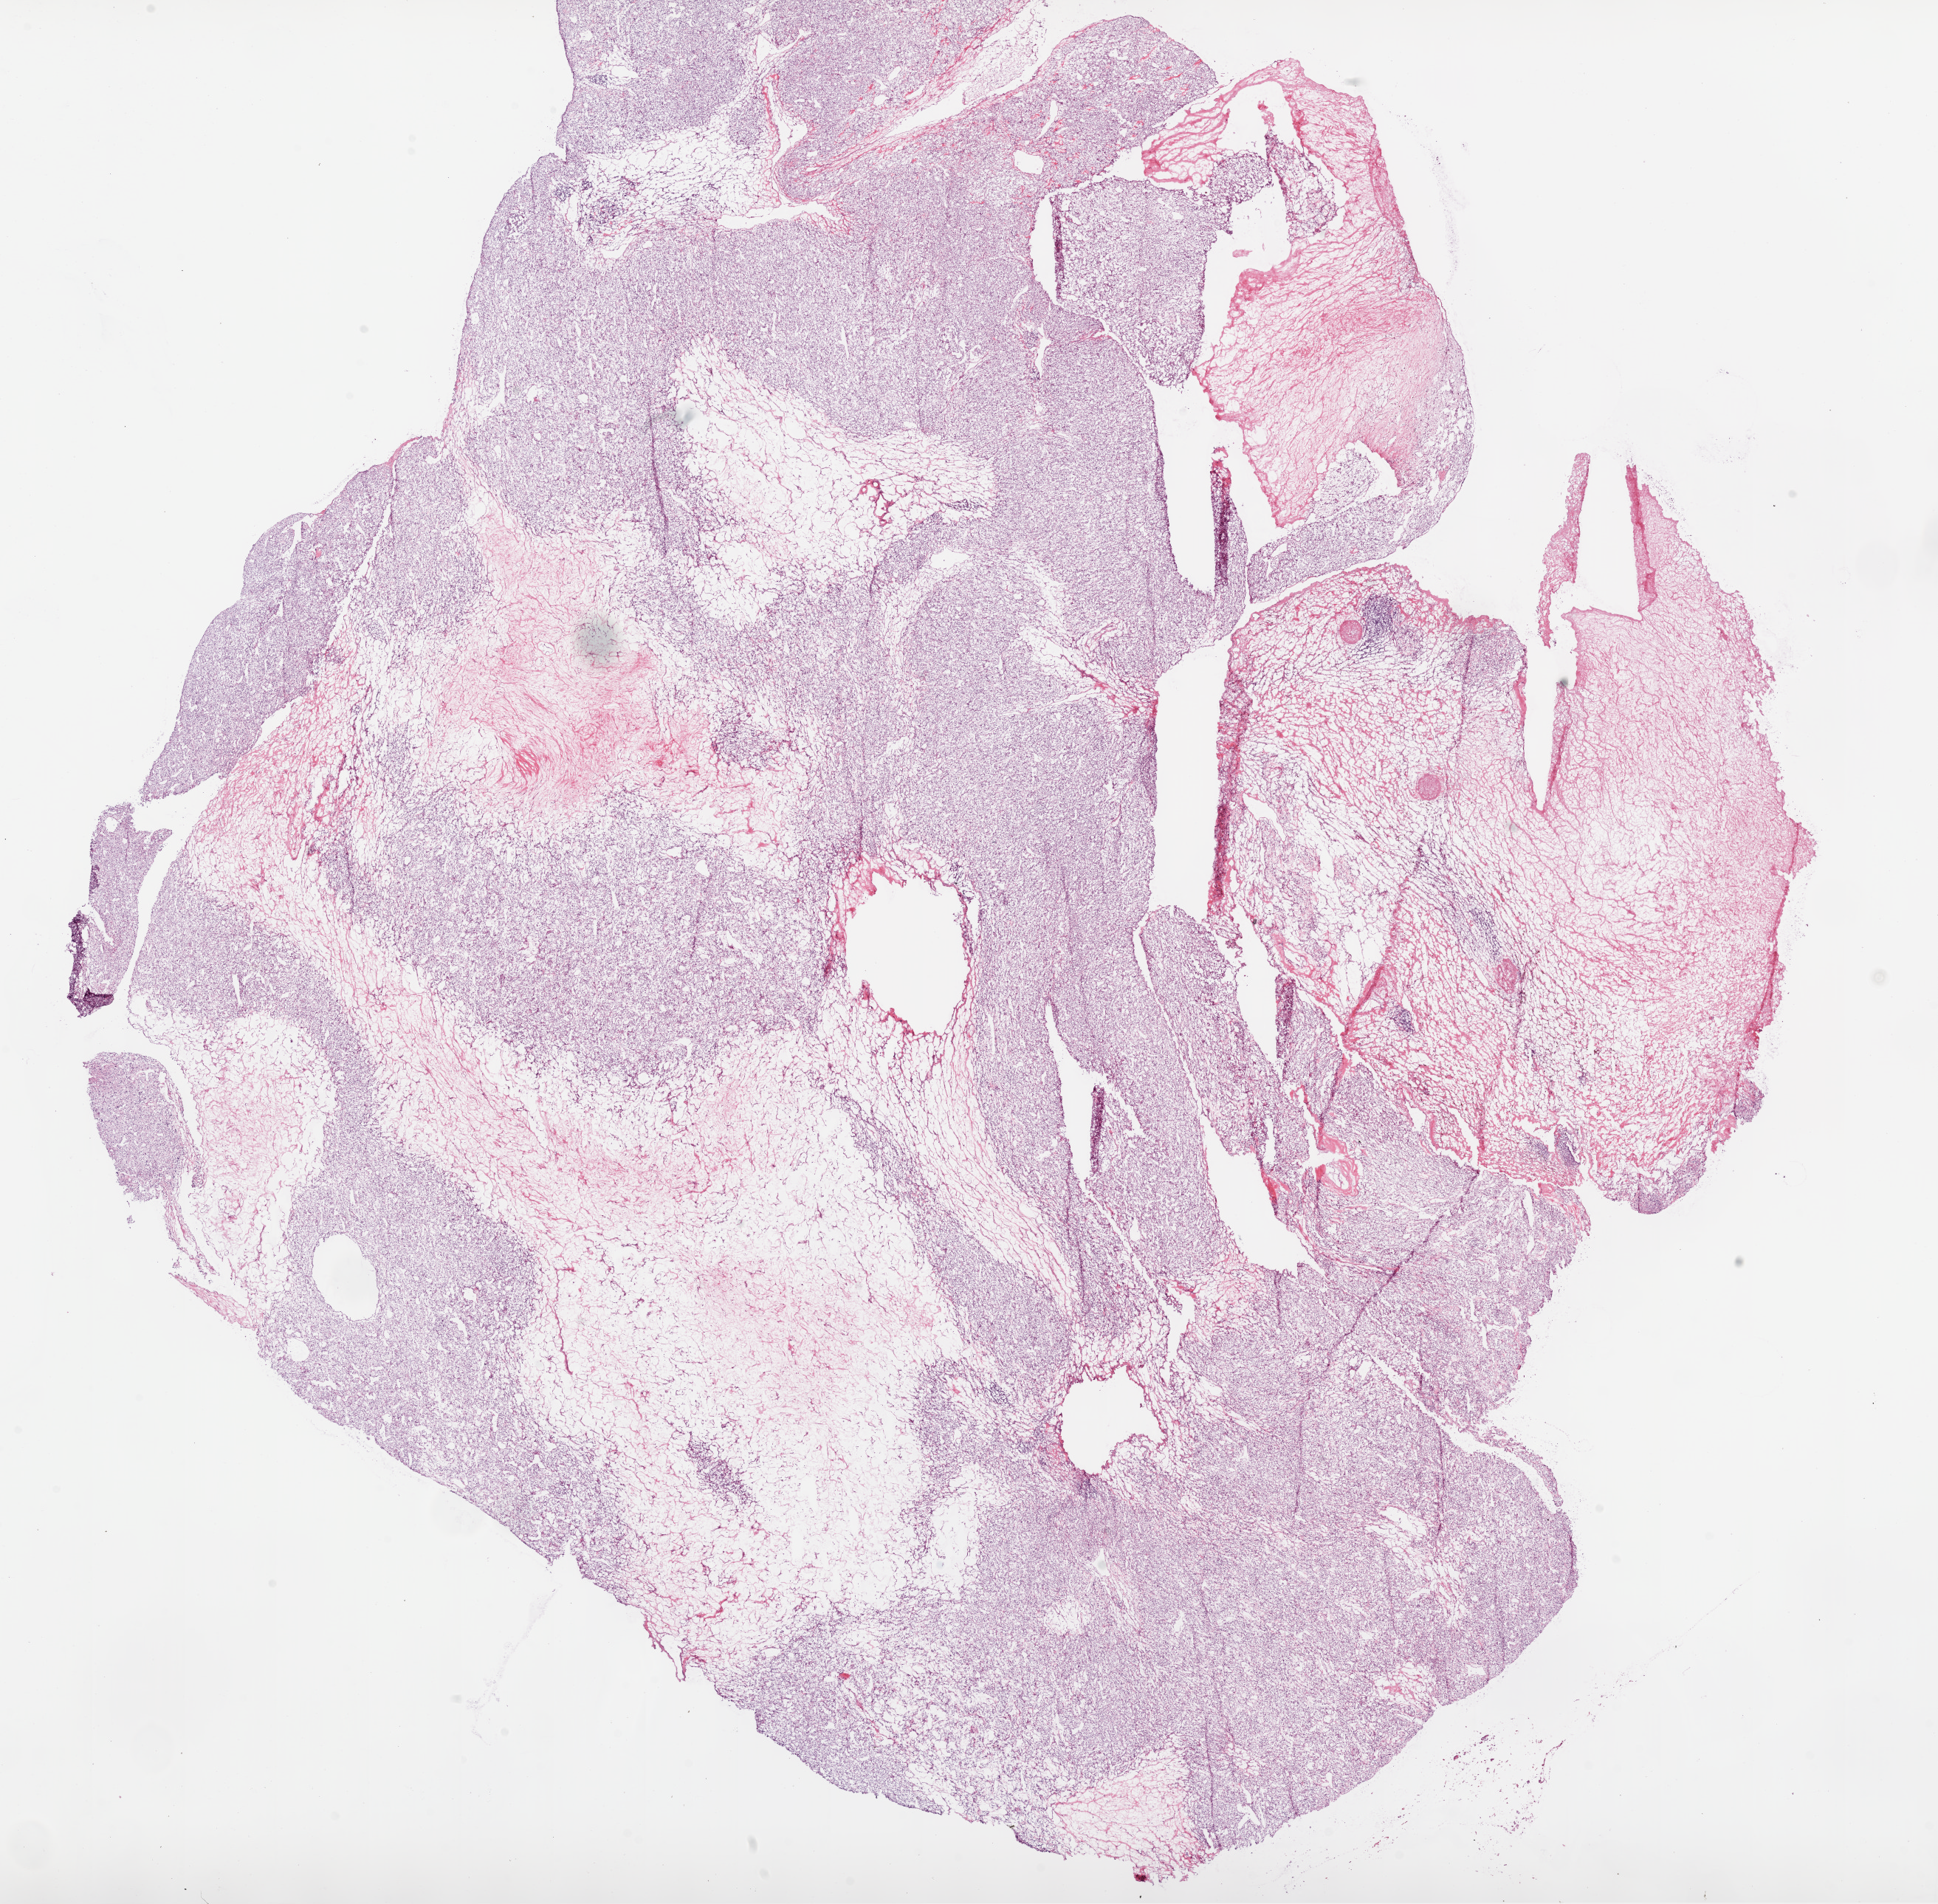
Hematoxylin and eosin (H&E) stained whole-slide image, whole scanned area (about 21.1 x 20.7 mm, from a 20x scan) shown as a low-resolution overview, frozen section, primary tumour sample from the kidney. Female, age 69 years at initial diagnosis. Histologic grade: G2 (moderately differentiated). Composition of this section per pathologist review: tumour cells 65%, tumour nuclei 80%, normal cells 0%, stromal cells 35%, necrosis 0%.
Lymph nodes positive (case pathology): 0 of 3 examined. Histologic diagnosis: Clear cell adenocarcinoma, NOS. TNM: T3a N0 M0. Laterality: right. AJCC pathologic stage: III (7th edition).